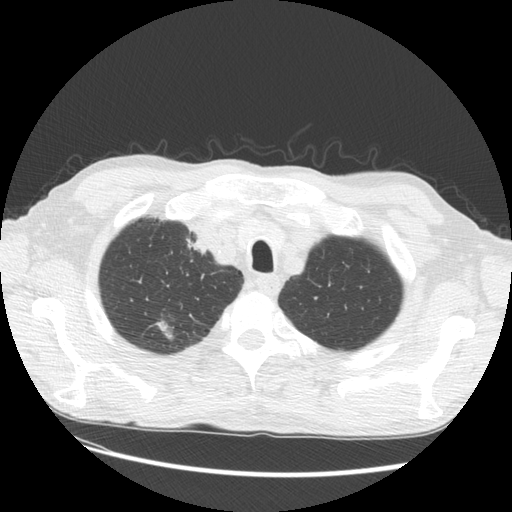
Low-dose screening chest CT, one axial slice. Slice 118 of 133 in the series (ordered by position). Reconstruction kernel STANDARD. 120 kVp. Lung window (W 1500 / L -600 HU). 2.5 mm slice thickness. 512 × 512 image matrix, field of view 360 × 360 mm.
Structures marked on this image (manually delineated by an expert):
- lesion 2 (tumor, upper lobe of right lung): bounding box <154,320,174,340> (left, top, right, bottom; pixels)